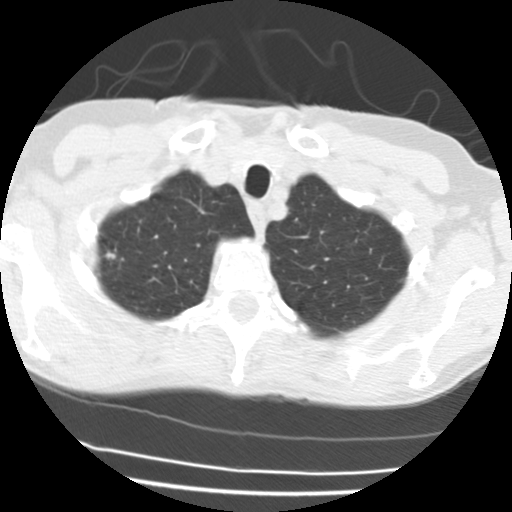
Axial slice from a low-dose chest CT screening exam. Third screening round (two years after baseline). Lung window (W 1500 / L -600 HU). 2.5 mm slice thickness. Slice 182 of 195 in the series. Female, age 58 years at enrolment. Current smoker at enrolment.
Expert reader's lesion annotation, bounding box (x1, y1, x2, y2) in pixels: (86, 240, 125, 276). The screening reader recorded 3 non-calcified nodules or masses ≥4 mm on this exam; which of them this box marks is not recorded.